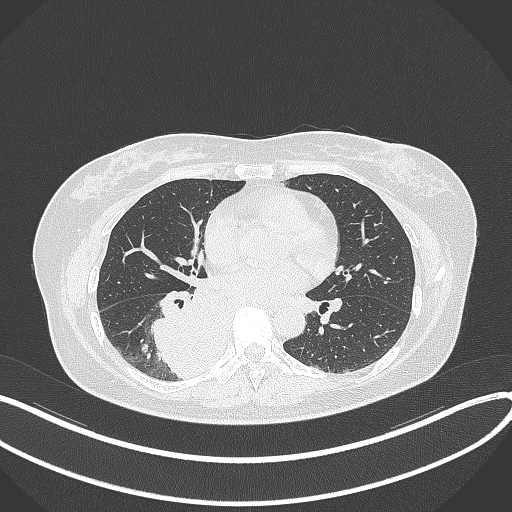
Chest CT, one axial slice. Position 167 of 331 along the scan axis. Reconstruction kernel B70f. 120 kVp. Lung window (W 1500 / L -600 HU). 512 × 512 image matrix, field of view 400 × 400 mm. Patient: female, 54 years. Case-level facts recorded for this patient, not image findings: clinical TNM (as recorded): T4 N0 M0.
Structures marked on this image (rectangle marked by the reading radiologist):
- lung tumour (recorded histology: adenocarcinoma): bounding box (x1, y1, x2, y2) in pixels: (146, 285, 220, 378)